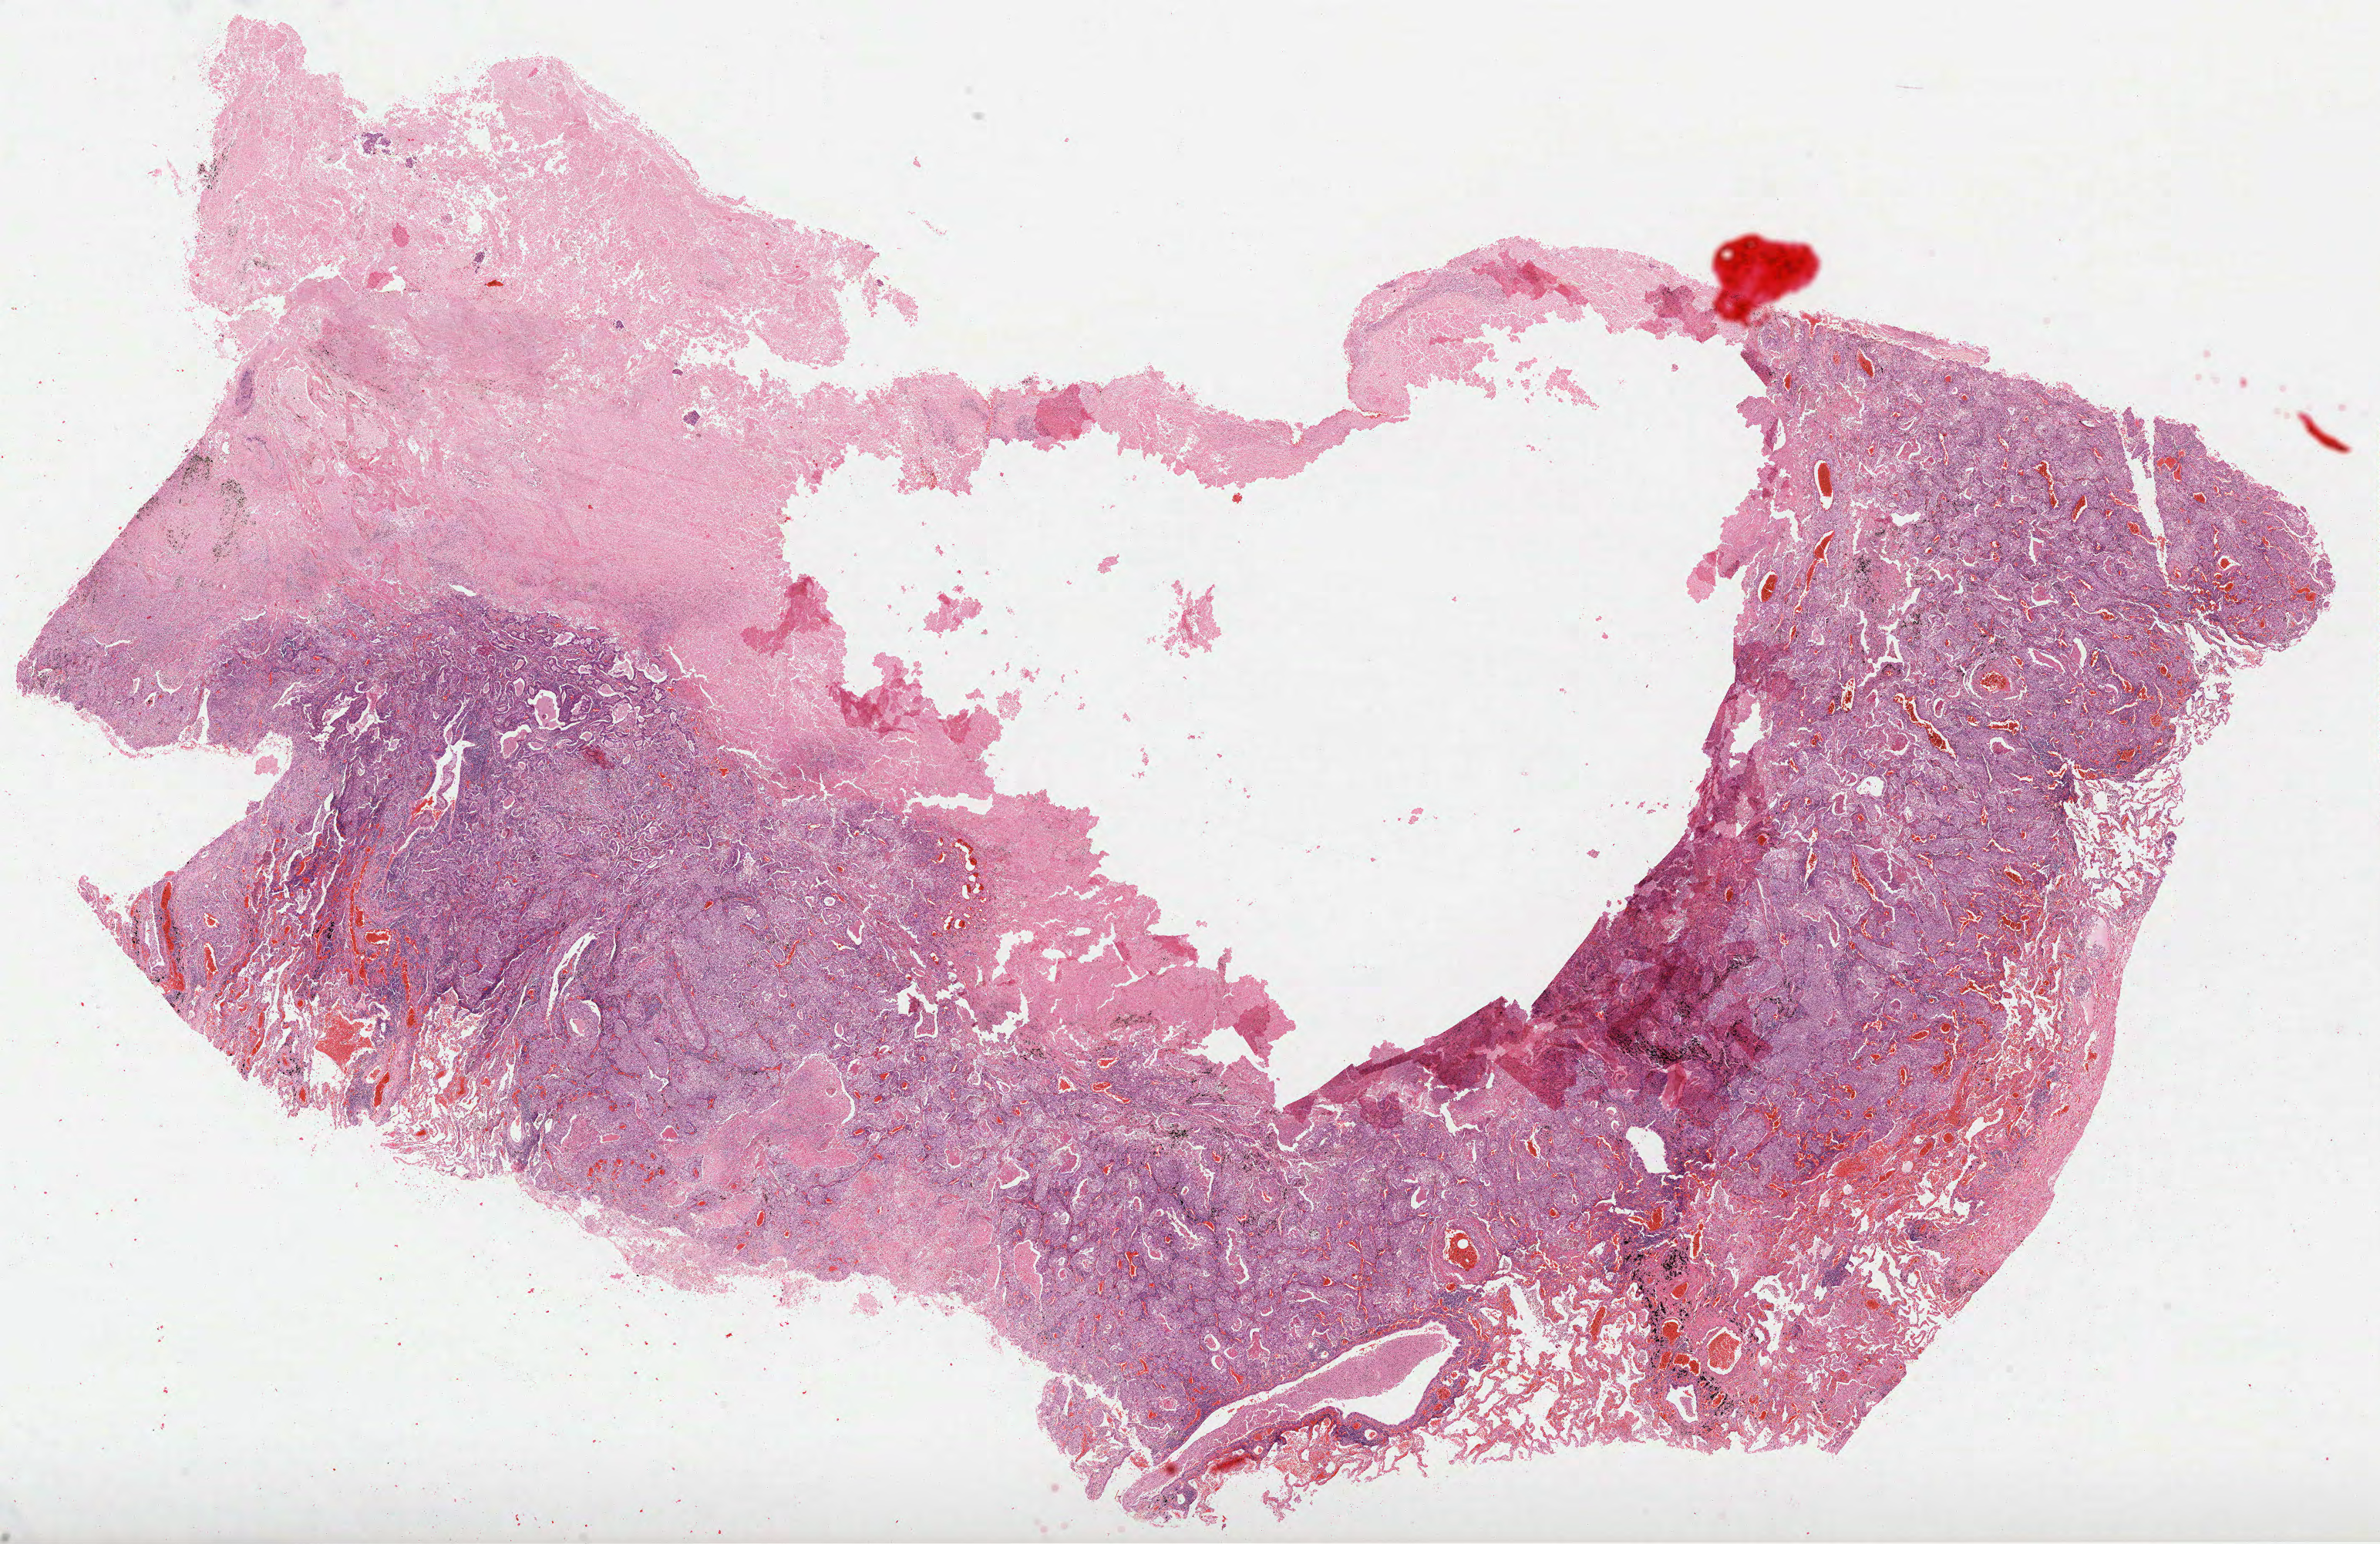
Whole-slide histology image, Hematoxylin and eosin (H&E) stained — whole scanned area (about 24.9 x 16.2 mm) shown as a low-resolution overview; formalin-fixed paraffin-embedded (FFPE) diagnostic section; sample: primary tumour, lung. Male, age 71 years at initial diagnosis.
Histologic diagnosis: Papillary squamous cell carcinoma (upper lobe, lung).